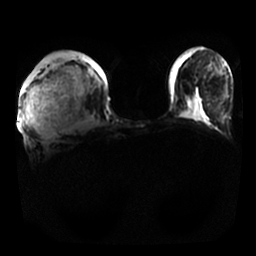
Breast MRI, one axial slice; position 5 of 25 along the scan axis; diffusion-weighted series; image 2 of 4 stored at this slice position (different b-values; order by instance number); 1.5 T; 4 mm slice thickness; 256 × 256 image matrix, field of view 350 × 350 mm. Female patient.
Annotated regions visible in this slice (outlined manually by an expert reader):
- tumour on diffusion-weighted imaging: bounding box <29,83,50,132> (left, top, right, bottom; pixels)